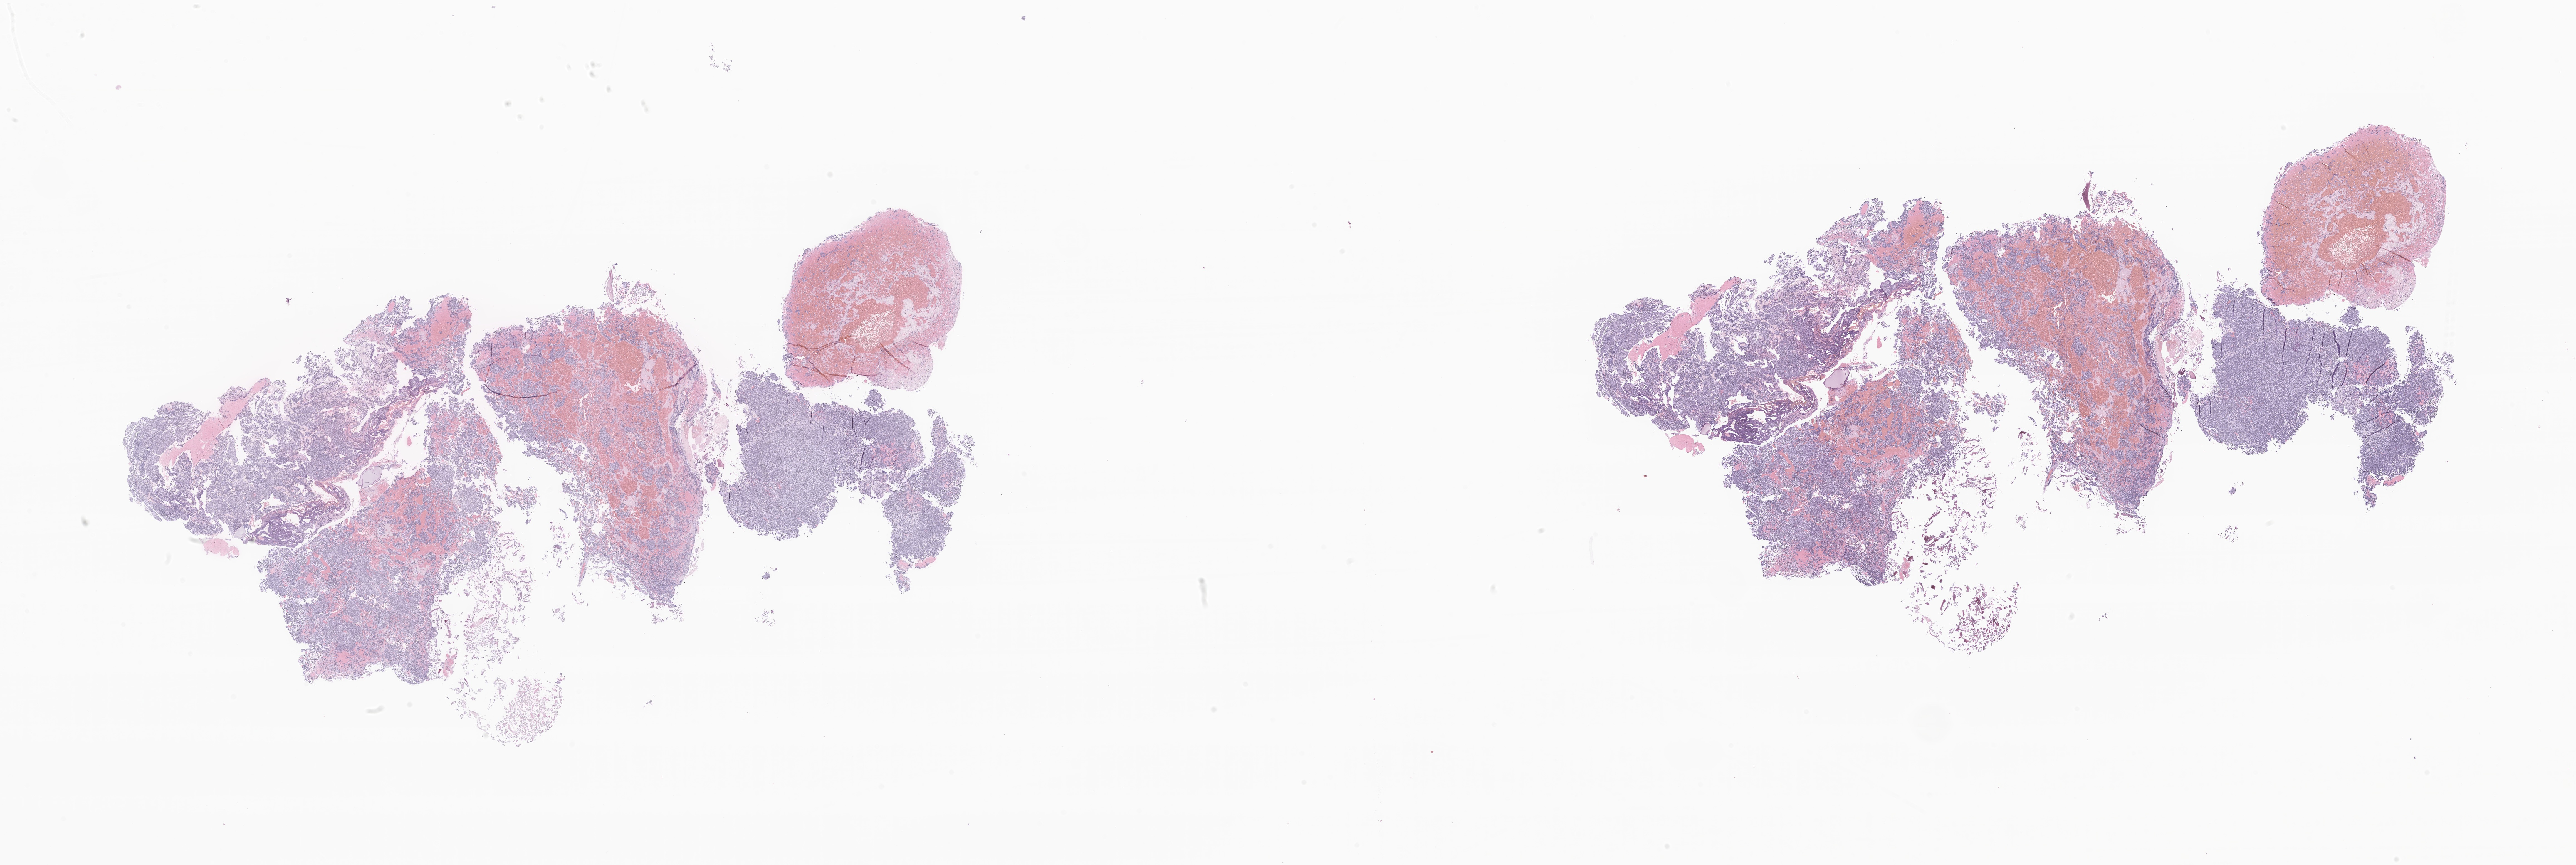
Digitized hematoxylin and eosin (H&E)-stained section of tumor tissue from the brain — whole scanned area (about 39.0 x 13.1 mm) shown as a low-resolution overview, formalin-fixed, paraffin-embedded (FFPE) tissue. Patient: female, age 178 months (14 years 10 months).
Recorded diagnosis: Medulloblastoma, NOS.